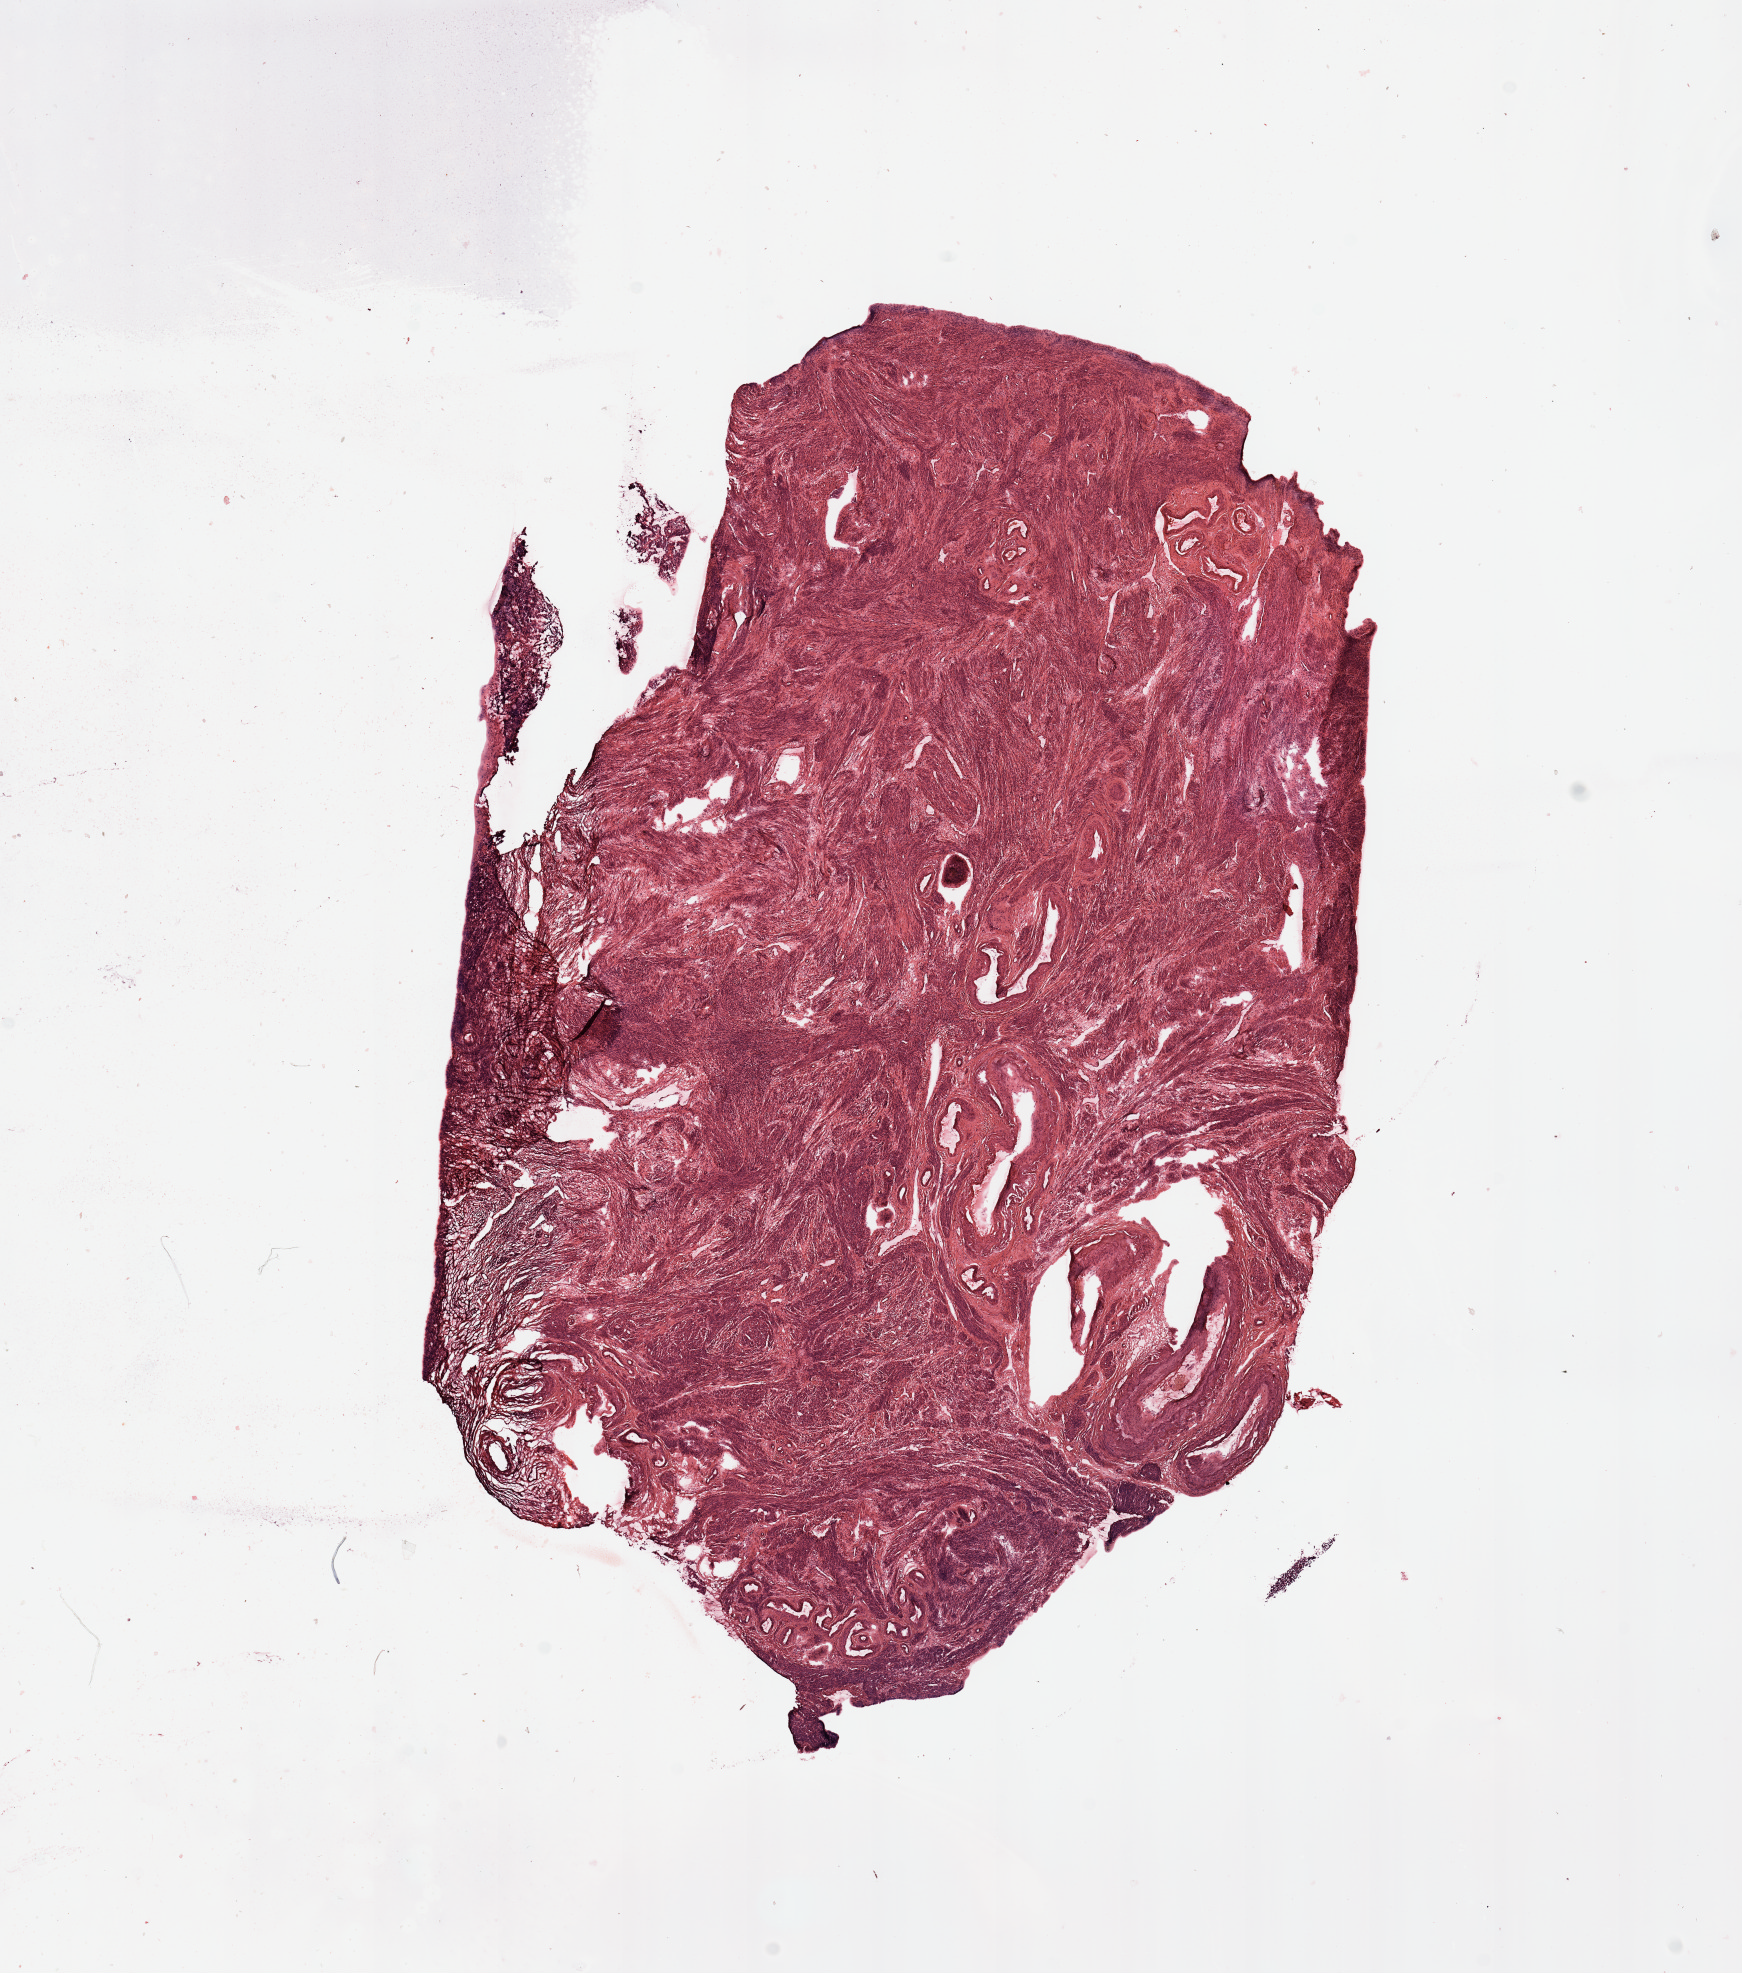
H&E whole-slide image — a low-resolution overview of the entire scanned area, about 13.8 x 15.6 mm (slide scanned at 20x). Tumour tissue sample, uterus. Female, 70 y/o. Histologic grade: G2 (moderately differentiated).
AJCC pathologic stage: I. Histologic diagnosis: Endometrioid adenocarcinoma, NOS.